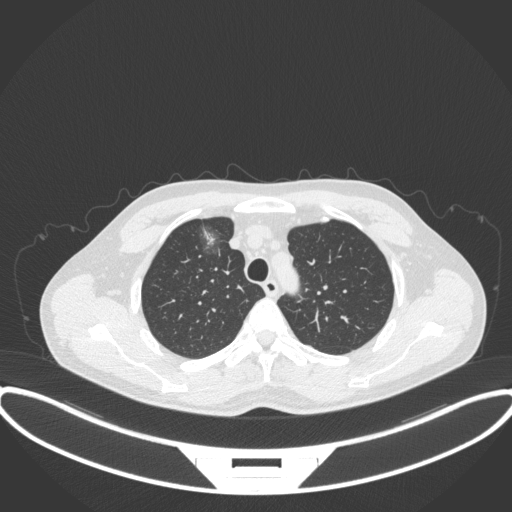
Chest CT, one axial slice. Position 290 of 395 along the scan axis. Reconstruction kernel B31f. Lung window (W 1500 / L -600 HU). 1 mm slice thickness. 512 × 512 image matrix, field of view 424 × 424 mm. Male patient, age 60 years. From the clinical record (not read from this slice): clinical TNM (as recorded): T1c N0 M0.
Outlined on this slice (bounding box drawn by a radiologist):
- lung tumour (recorded histology: adenocarcinoma): bounding box [x1, y1, x2, y2] px = [194, 217, 225, 262]